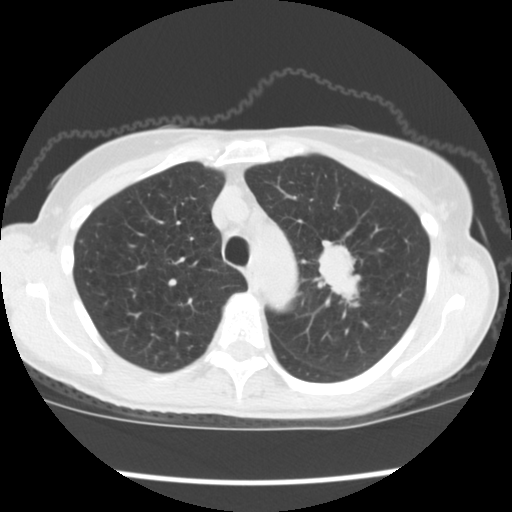
Chest CT (low-dose screening protocol), one axial image; first (baseline) screen; lung window (W 1500 / L -600 HU); 512 × 512 image matrix. Female, age 67 years at enrolment. Former smoker at enrolment.
- Expert-annotated lung lesion, bounding box <306,234,379,311> (left, top, right, bottom; pixels).
- Screening reader's record for this exam (one nodule recorded; not confirmed to be the boxed lesion): non-calcified nodule or mass ≥4 mm, left upper lobe, 34 × 32 mm, spiculated (stellate) margins, soft tissue attenuation, pre-existing on the prior screen: no.
- Participant outcome: lung cancer diagnosed 17 days after this screen — small cell carcinoma, NOS, left upper lobe, stage IIIA (AJCC 6th edition), 40 mm at pathology.